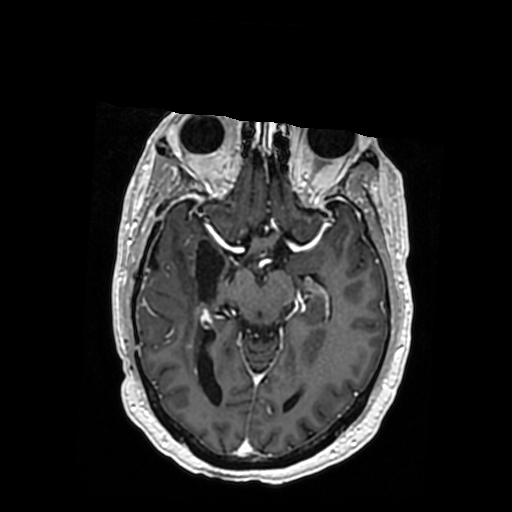
Brain MRI from a brain-tumour surgery series, one axial slice; slice 207 of 364 in the series (ordered by position); T1-weighted post-contrast; 0.5 mm slice thickness; 512 × 512 image matrix, field of view 260 × 260 mm. Case-level facts recorded for this patient, not image findings: histopathology: Oligodendroglioma; WHO grade: 3; IDH mutation: yes; tumour location: Right Posterior Temporal Inferior Parietal.
Annotated regions visible in this slice (expert manual segmentation):
- previous resection cavity: bounding box <150,239,236,301> (left, top, right, bottom; pixels)